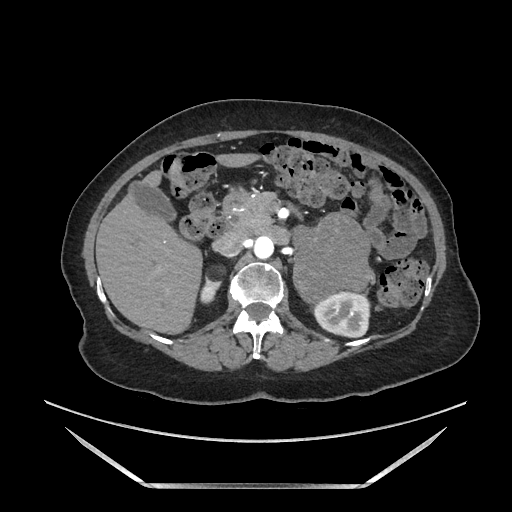
Contrast-enhanced abdominal CT, one axial slice; position 97 of 205 along the scan axis; soft-tissue window (W 400 / L 40 HU); 1.25 mm slice thickness; 512 × 512 image matrix. Female patient. Case-level facts recorded for this patient, not image findings: diagnosis: adrenocortical carcinoma; tumour side: left adrenal; tumour size at pathology: 12.5 cm; Ki-67 index: 39 %; stage (as recorded): 3.
Outlined on this slice (semi-automatically segmented with operator editing):
- mass: bounding box <296,215,370,299> (left, top, right, bottom; pixels)